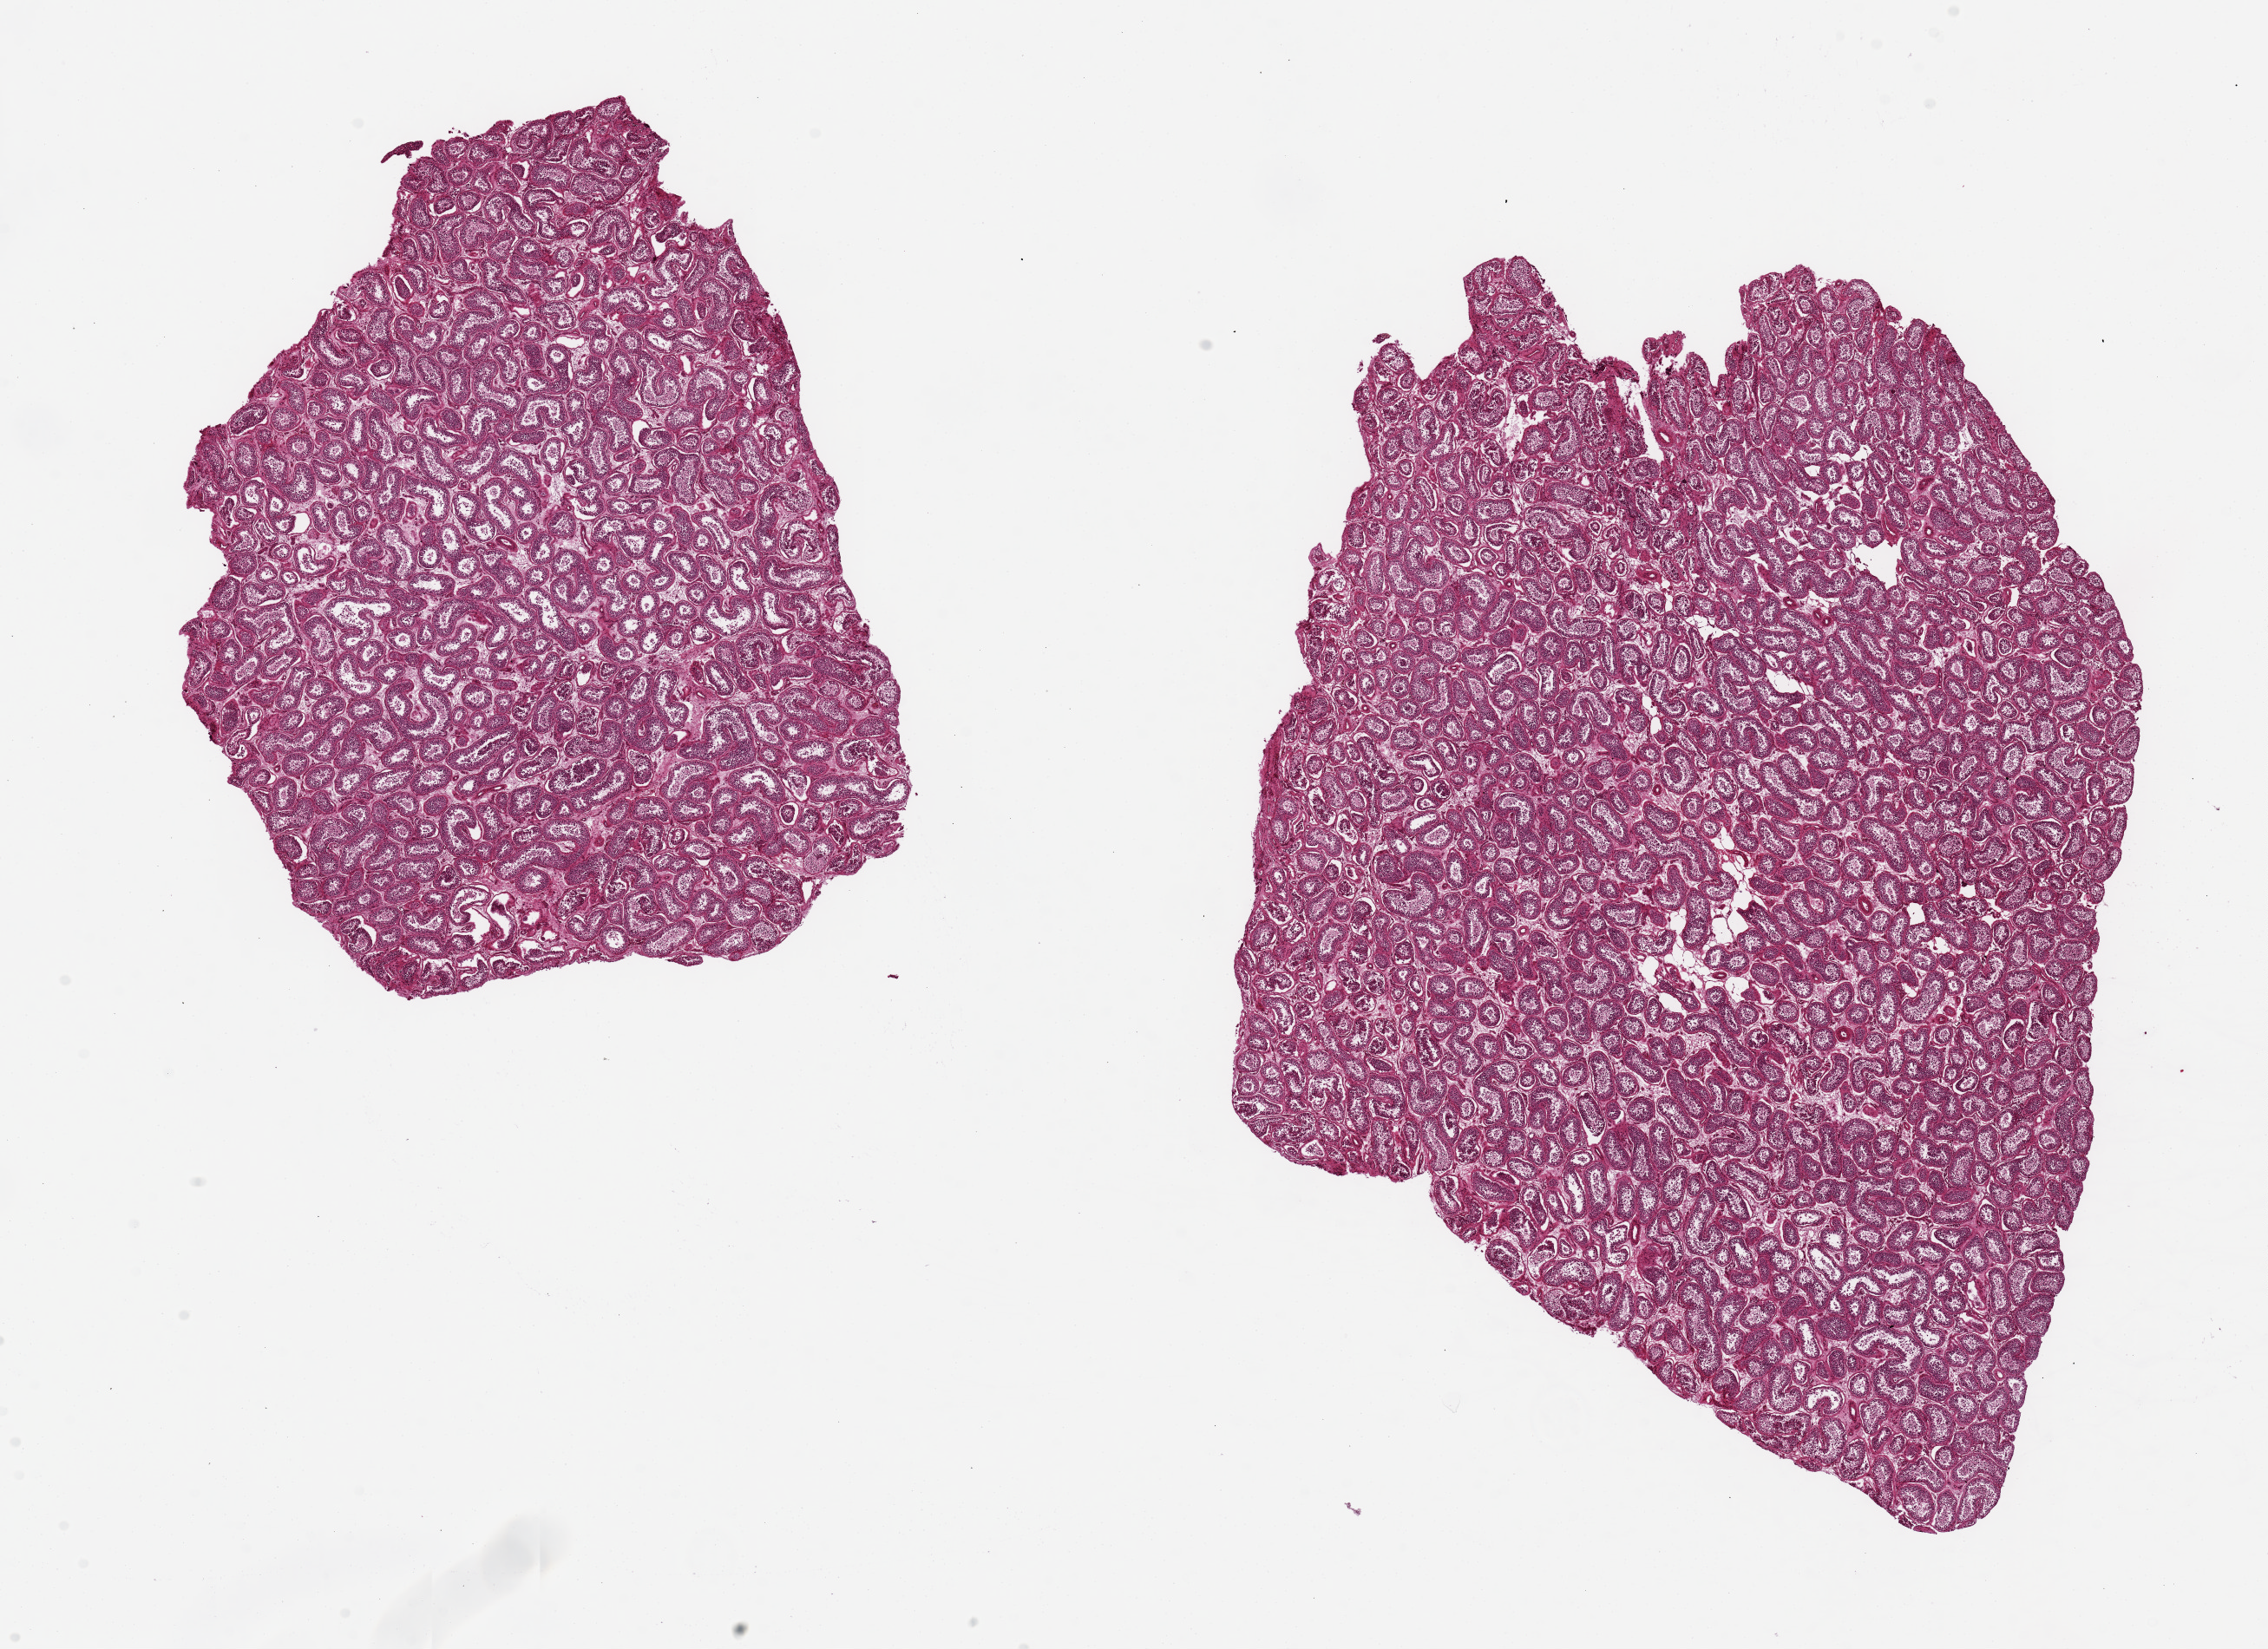
Digitized H&E-stained section, low-resolution overview of the scanned area, about 20.7 x 15.0 mm (acquisition: 20x scan), PAXgene-fixed paraffin-embedded (PFPE) section, section of testis (target tissue), donor tissue sample. Donor: male.
Pathologist's review note for this sample: 2 pieces, 7.6x5.3 & 8x11 mm; spermatogenesis.